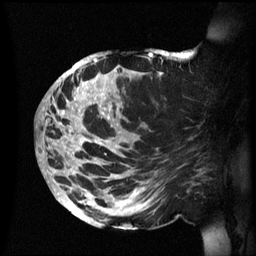
Breast MRI (dynamic contrast-enhanced), one sagittal slice; position 31 of 60 along the scan axis; dynamic contrast-enhanced series, image 2 of 3 at this slice position (ordered by acquisition); 1.5 T; TE 4.2 ms, TR 8.4 ms; 2.4 mm slice thickness; 256 × 256 image matrix, field of view 230 × 230 mm. Female patient, age 48 years.
Structures marked on this image (semi-automatically segmented with operator editing):
- analysis volume of interest (the breast-tissue region the enhancement analysis was run in; not a lesion): bounding box (x1, y1, x2, y2) in pixels: (42, 49, 202, 230)
- tumour enhancement mask (voxels above the 70 % enhancement threshold inside the analysis volume of interest): (42, 52, 179, 223)